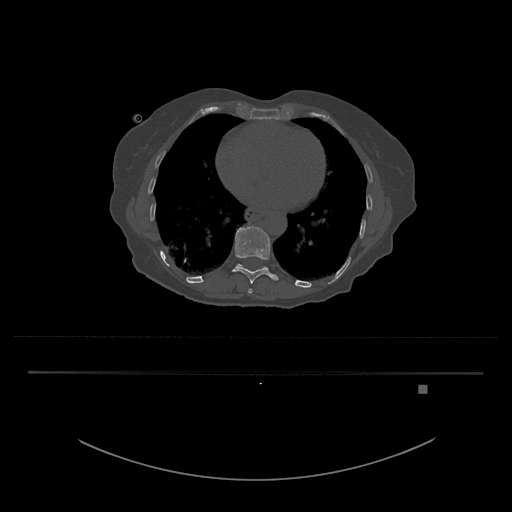
CT including the spine, one axial slice; position 708 of 797 along the scan axis; reconstruction kernel Br40s/3; bone window (W 1800 / L 400 HU); 512 × 512 image matrix. Patient: female, 57 years. From the clinical record (not read from this slice): primary cancer: cervical.
Annotated regions visible in this slice (semi-automatic segmentation, software-assisted and operator-edited):
- T10 vertebra: bounding box <232,225,278,285> (left, top, right, bottom; pixels)
- T11 vertebra: <237,264,267,268>
- T9 vertebra: <248,289,253,293>